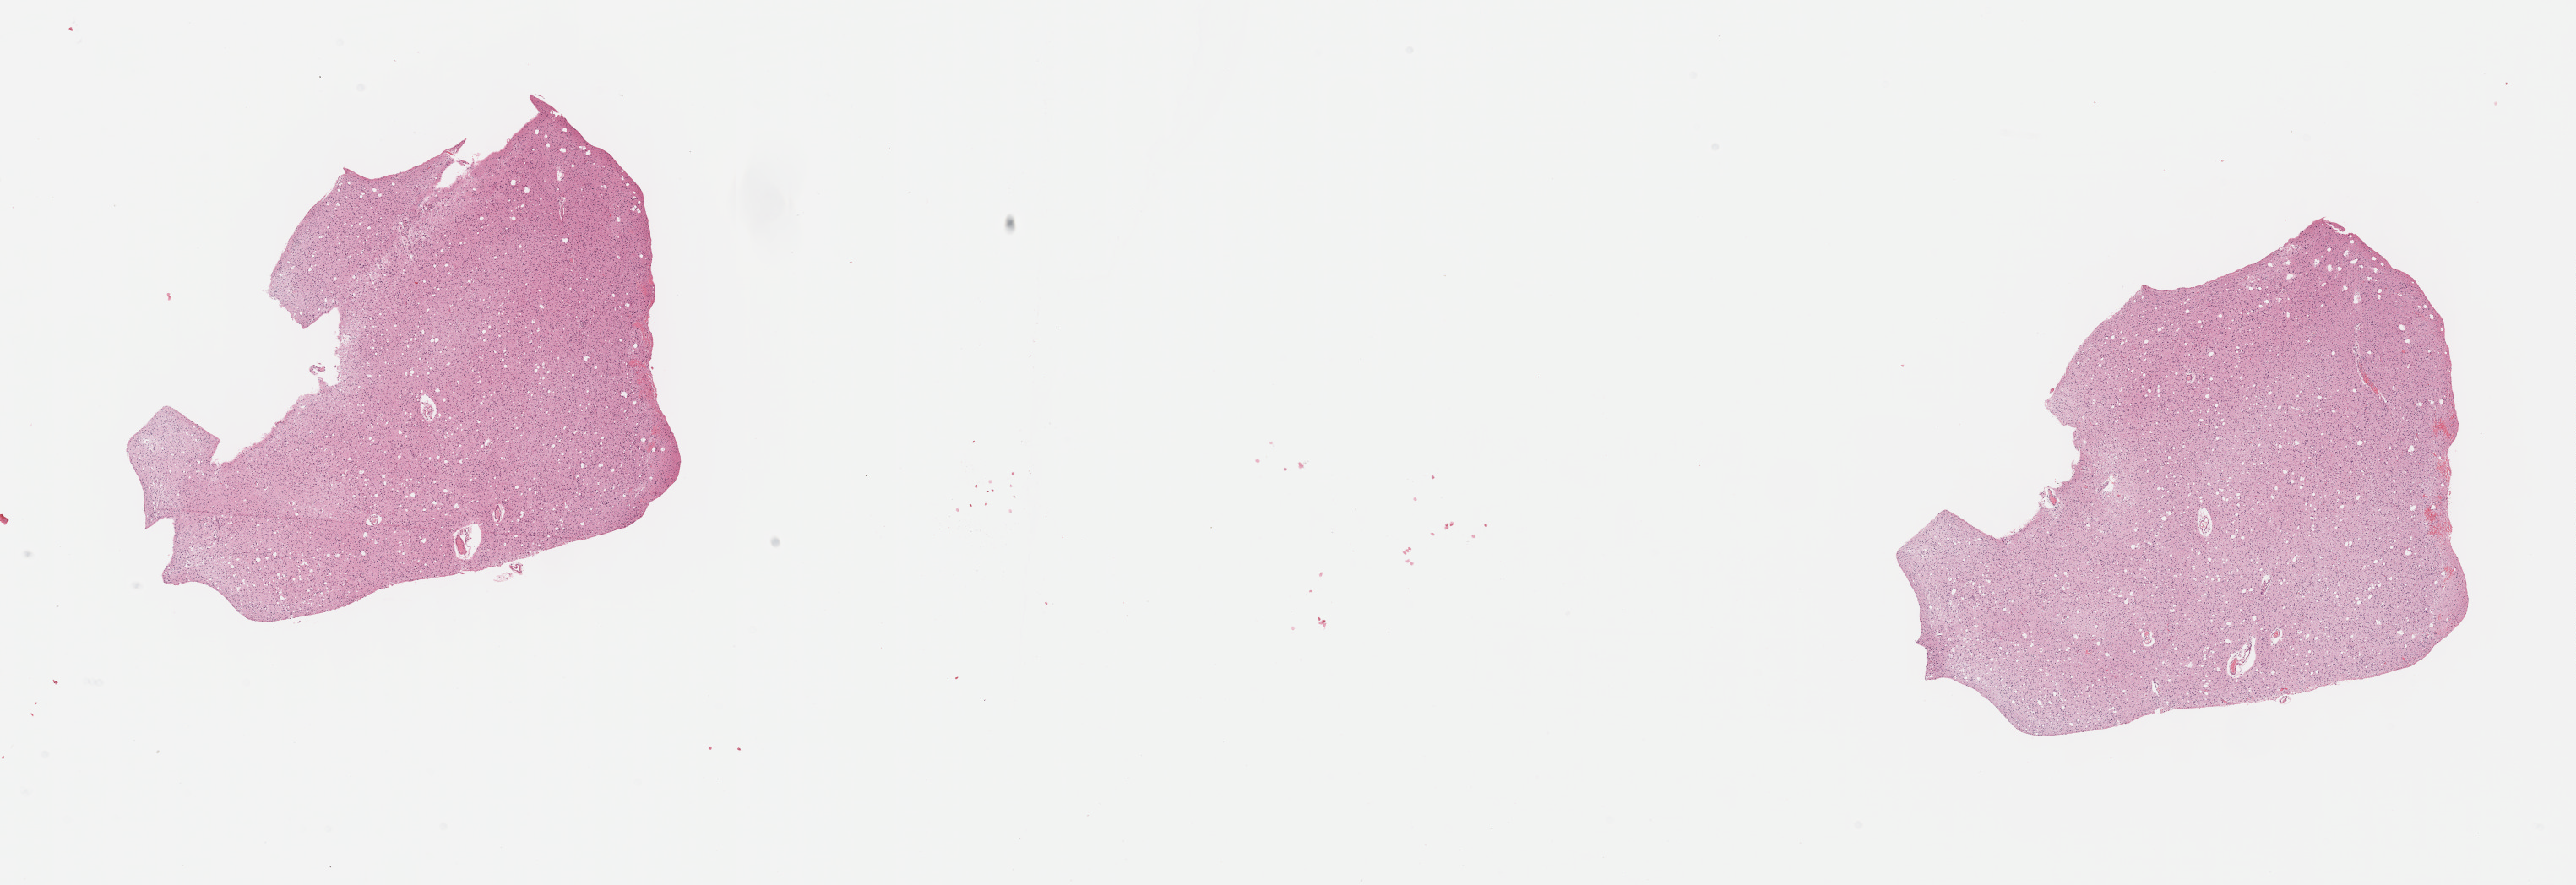
H&E whole-slide image, shown as a low-resolution overview of the whole scanned area (about 24.7 x 8.5 mm, from a 40x scan). Formalin-fixed paraffin-embedded (FFPE) diagnostic section. Brain, primary tumour sample. Female, age 20 years at initial diagnosis. Histologic grade: G2 (moderately differentiated).
Pathologic diagnosis: Oligodendroglioma, NOS (cerebrum).